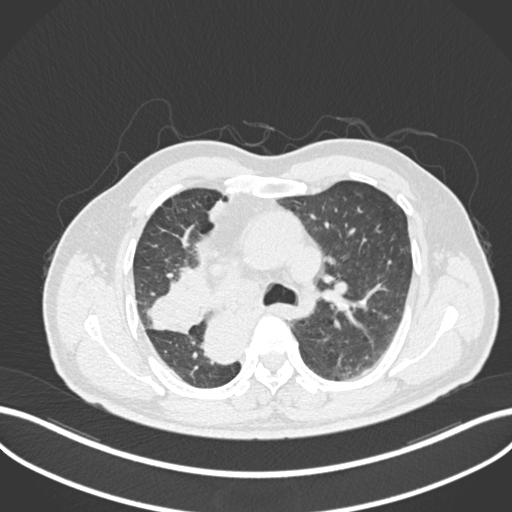
Chest CT, one axial slice. Slice 156 of 206 in the series (ordered by position). Lung window (W 1500 / L -600 HU). 1 mm slice thickness. 512 × 512 image matrix, field of view 400 × 400 mm. Male patient, age 67 years. Case-level facts recorded for this patient, not image findings: clinical TNM (as recorded): T2a N0 M0.
Outlined on this slice (bounding box drawn by a radiologist):
- lung tumour (recorded histology: squamous cell carcinoma): box from (x=146, y=278) to (x=210, y=336) px